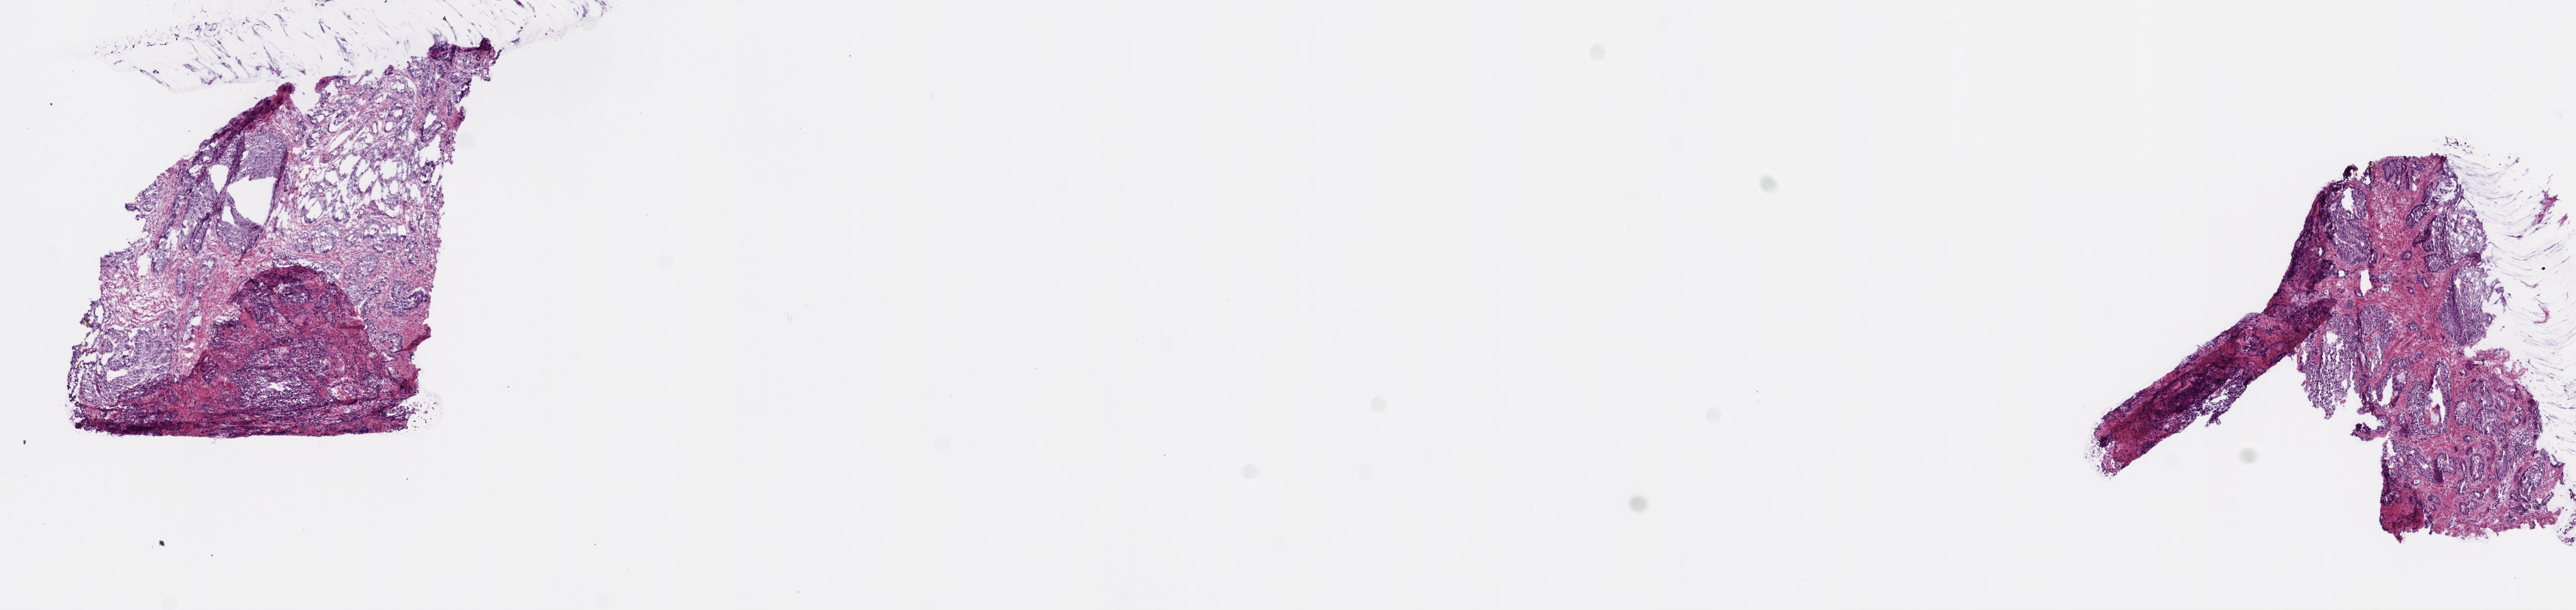
Digitized H&E tissue section (whole slide), whole scanned area (about 14.0 x 3.3 mm) shown as a low-resolution overview. Frozen section from the bottom of the tissue portion. Sample: primary tumour, prostate. Male, age 61 years at initial diagnosis. Gleason score: 7 (3+4). Slide review estimates, as recorded: tumour cells 75%, tumour nuclei 75%, normal cells 10%, stromal cells 15%, necrosis 0%. Inflammatory infiltration, as recorded: lymphocyte infiltration 0%, monocyte infiltration 0%, neutrophil infiltration 0%.
- histologic diagnosis: Acinar cell carcinoma (prostate gland)
- lymph nodes positive (case pathology): 0 of 4 examined